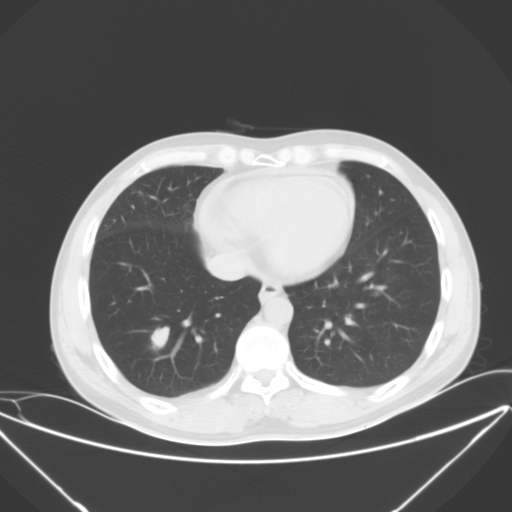
Chest CT, one axial slice. Slice 14 of 52 in the series (ordered by position). Lung window (W 1500 / L -600 HU). 5 mm slice thickness. 512 × 512 image matrix. Patient: male, 42 years. From the clinical record (not read from this slice): clinical TNM (as recorded): T1b N3 M1b.
Outlined on this slice (bounding box drawn by a radiologist):
- lung tumour (recorded histology: small cell carcinoma): bounding box <146,326,172,357> (left, top, right, bottom; pixels)